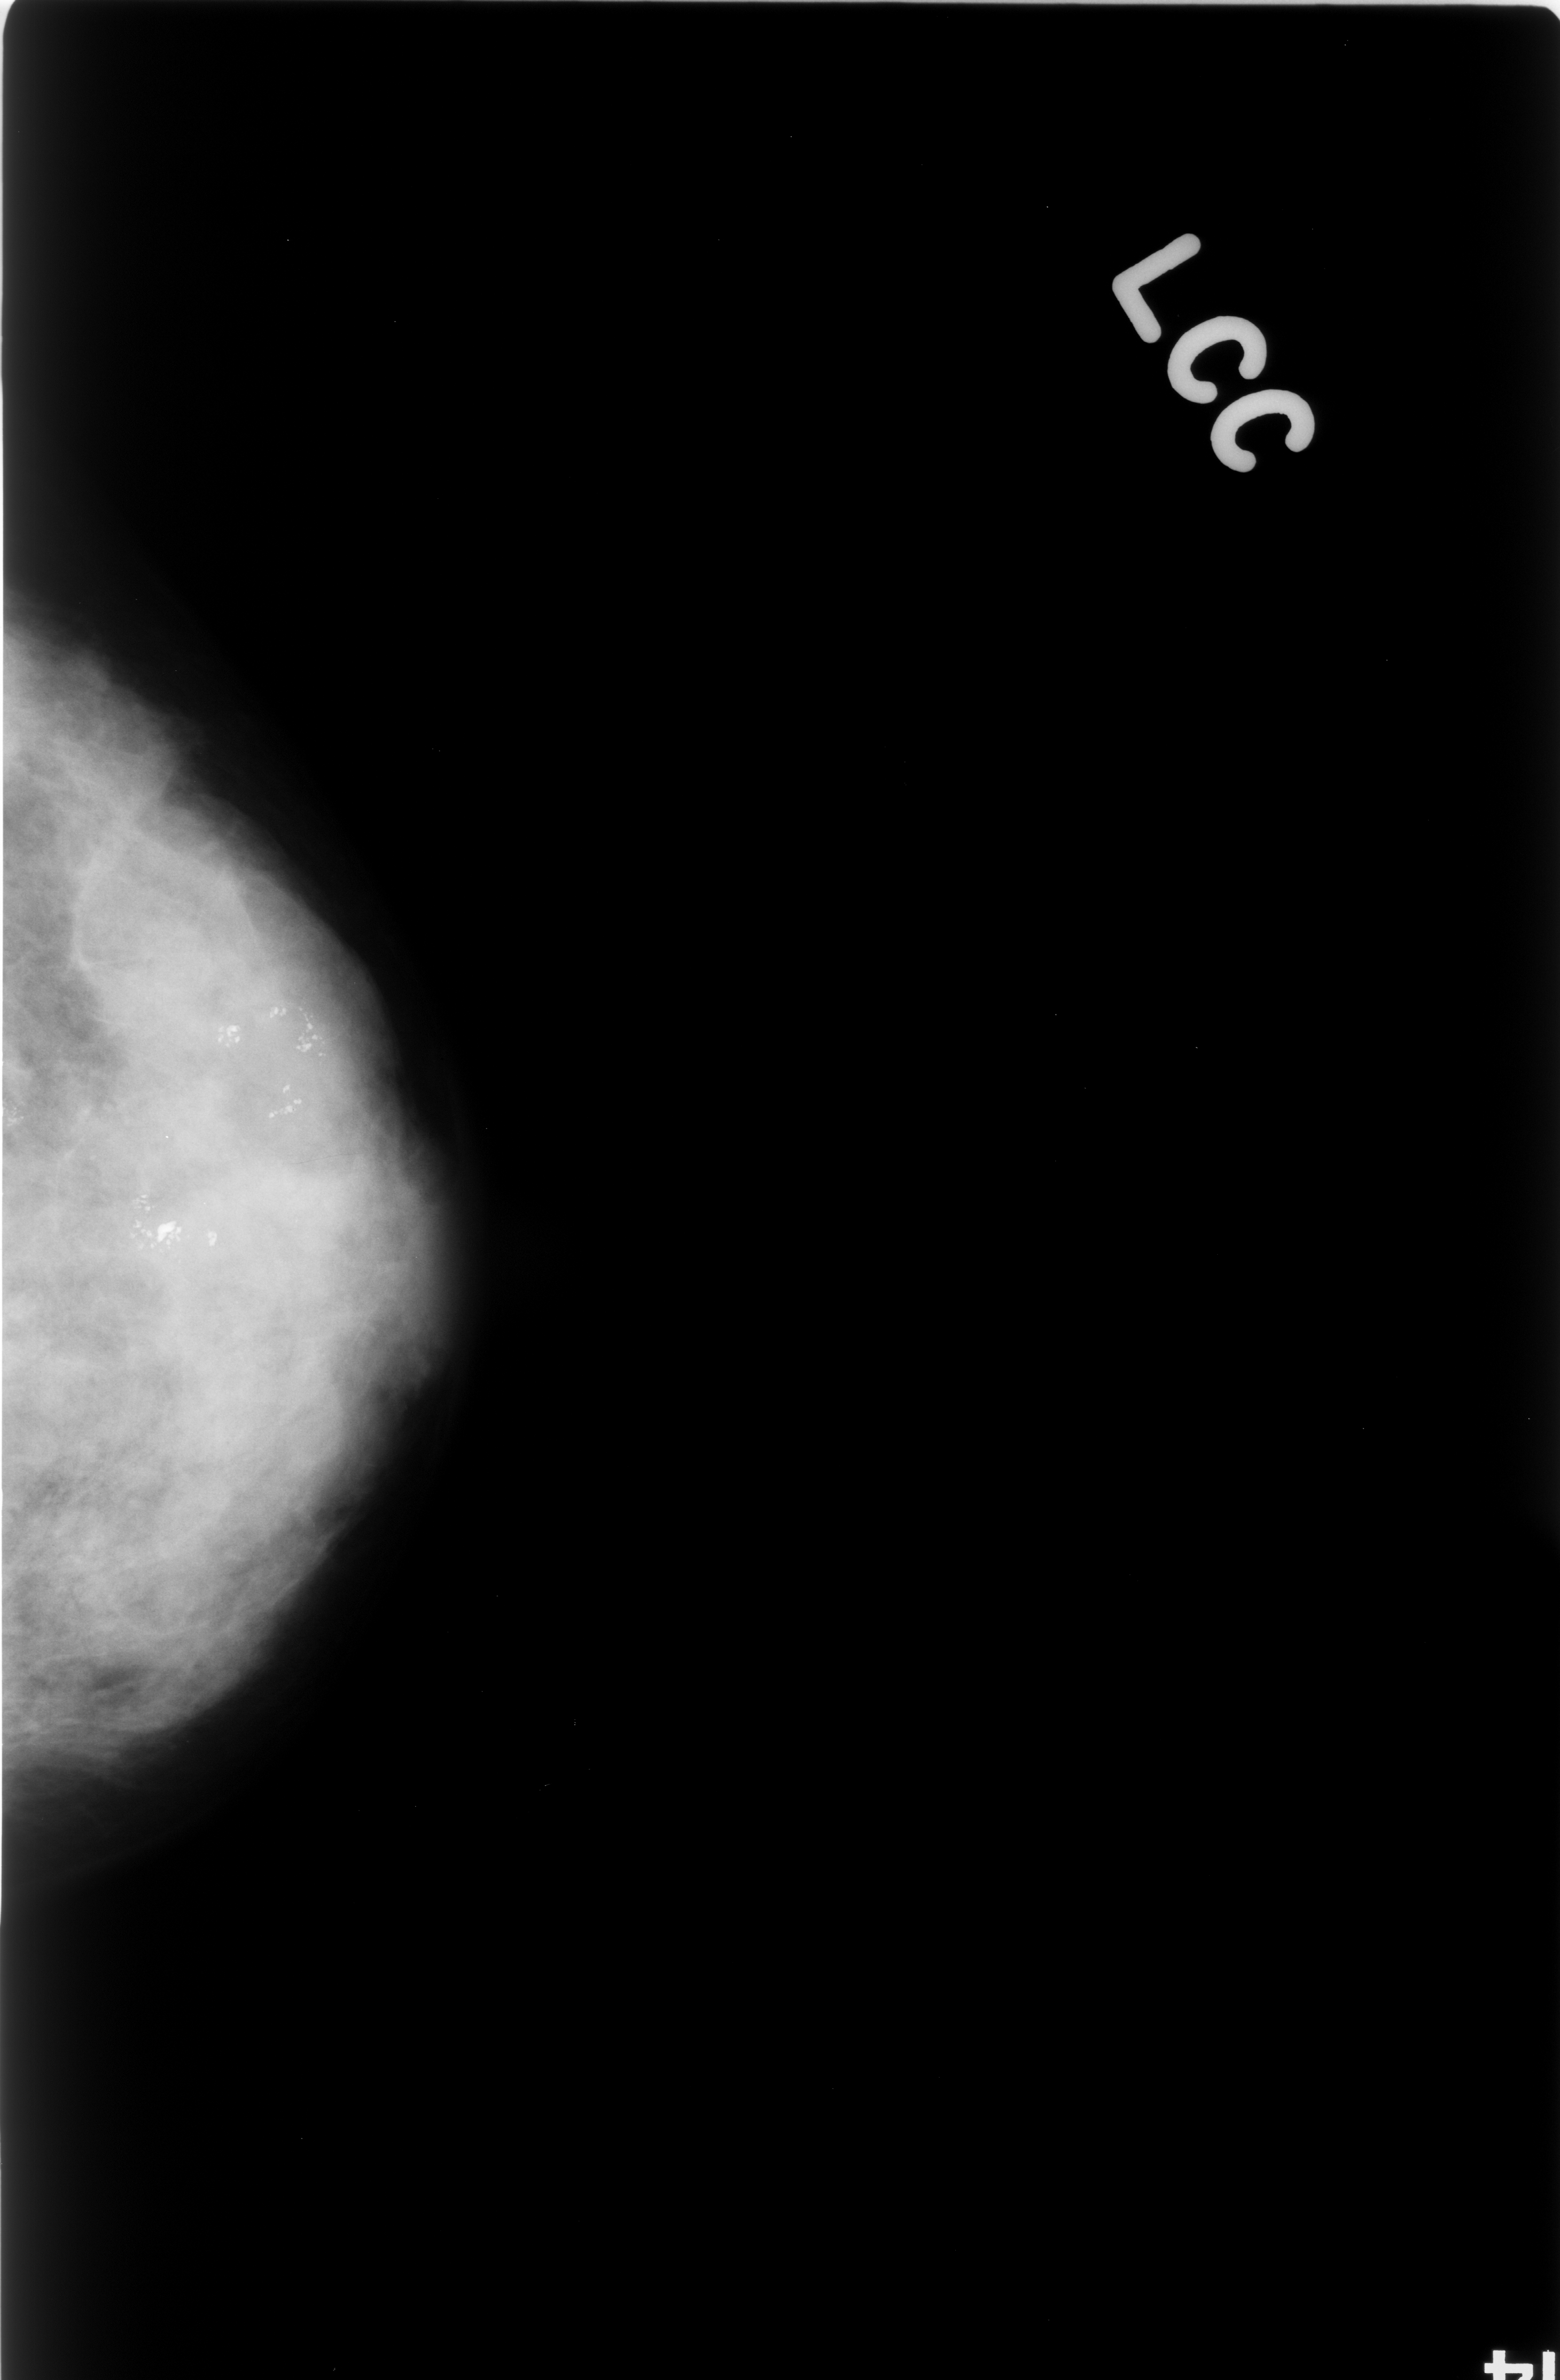
Mammogram (digitized film); left breast; craniocaudal (CC) view; breast composition: extremely dense (BI-RADS density category 4 of 4); 1560 × 2380 image matrix.
Expert-marked regions of interest on this image (one box per marked abnormality):
- Finding 1 of 3: calcifications, morphology pleomorphic, distribution clustered; BI-RADS assessment category 4; subtlety rating 5 on a 1 (subtle) to 5 (obvious) scale; pathology result (as recorded, not read from the image): benign: bounding box <0,1012,65,1168> (left, top, right, bottom; pixels)
- Finding 2 of 3: calcifications, morphology pleomorphic, distribution clustered; BI-RADS assessment category 4; subtlety rating 5 on a 1 (subtle) to 5 (obvious) scale; pathology result (as recorded, not read from the image): benign: <76,1149,257,1321>
- Finding 3 of 3: calcifications, morphology pleomorphic, distribution clustered; BI-RADS assessment category 4; pathology (as recorded): benign: <175,935,407,1150>